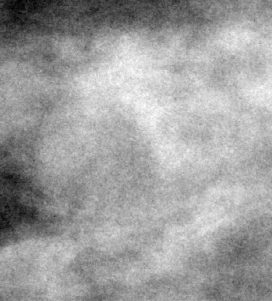
Cropped region of a digitized screen-film mammogram centred on a radiologist-marked abnormality, right breast, CC view, BI-RADS breast density category 2 (scale 1–4).
Mass, shape round / lobulated, margins circumscribed; BI-RADS assessment category 3; pathology (as recorded): benign.